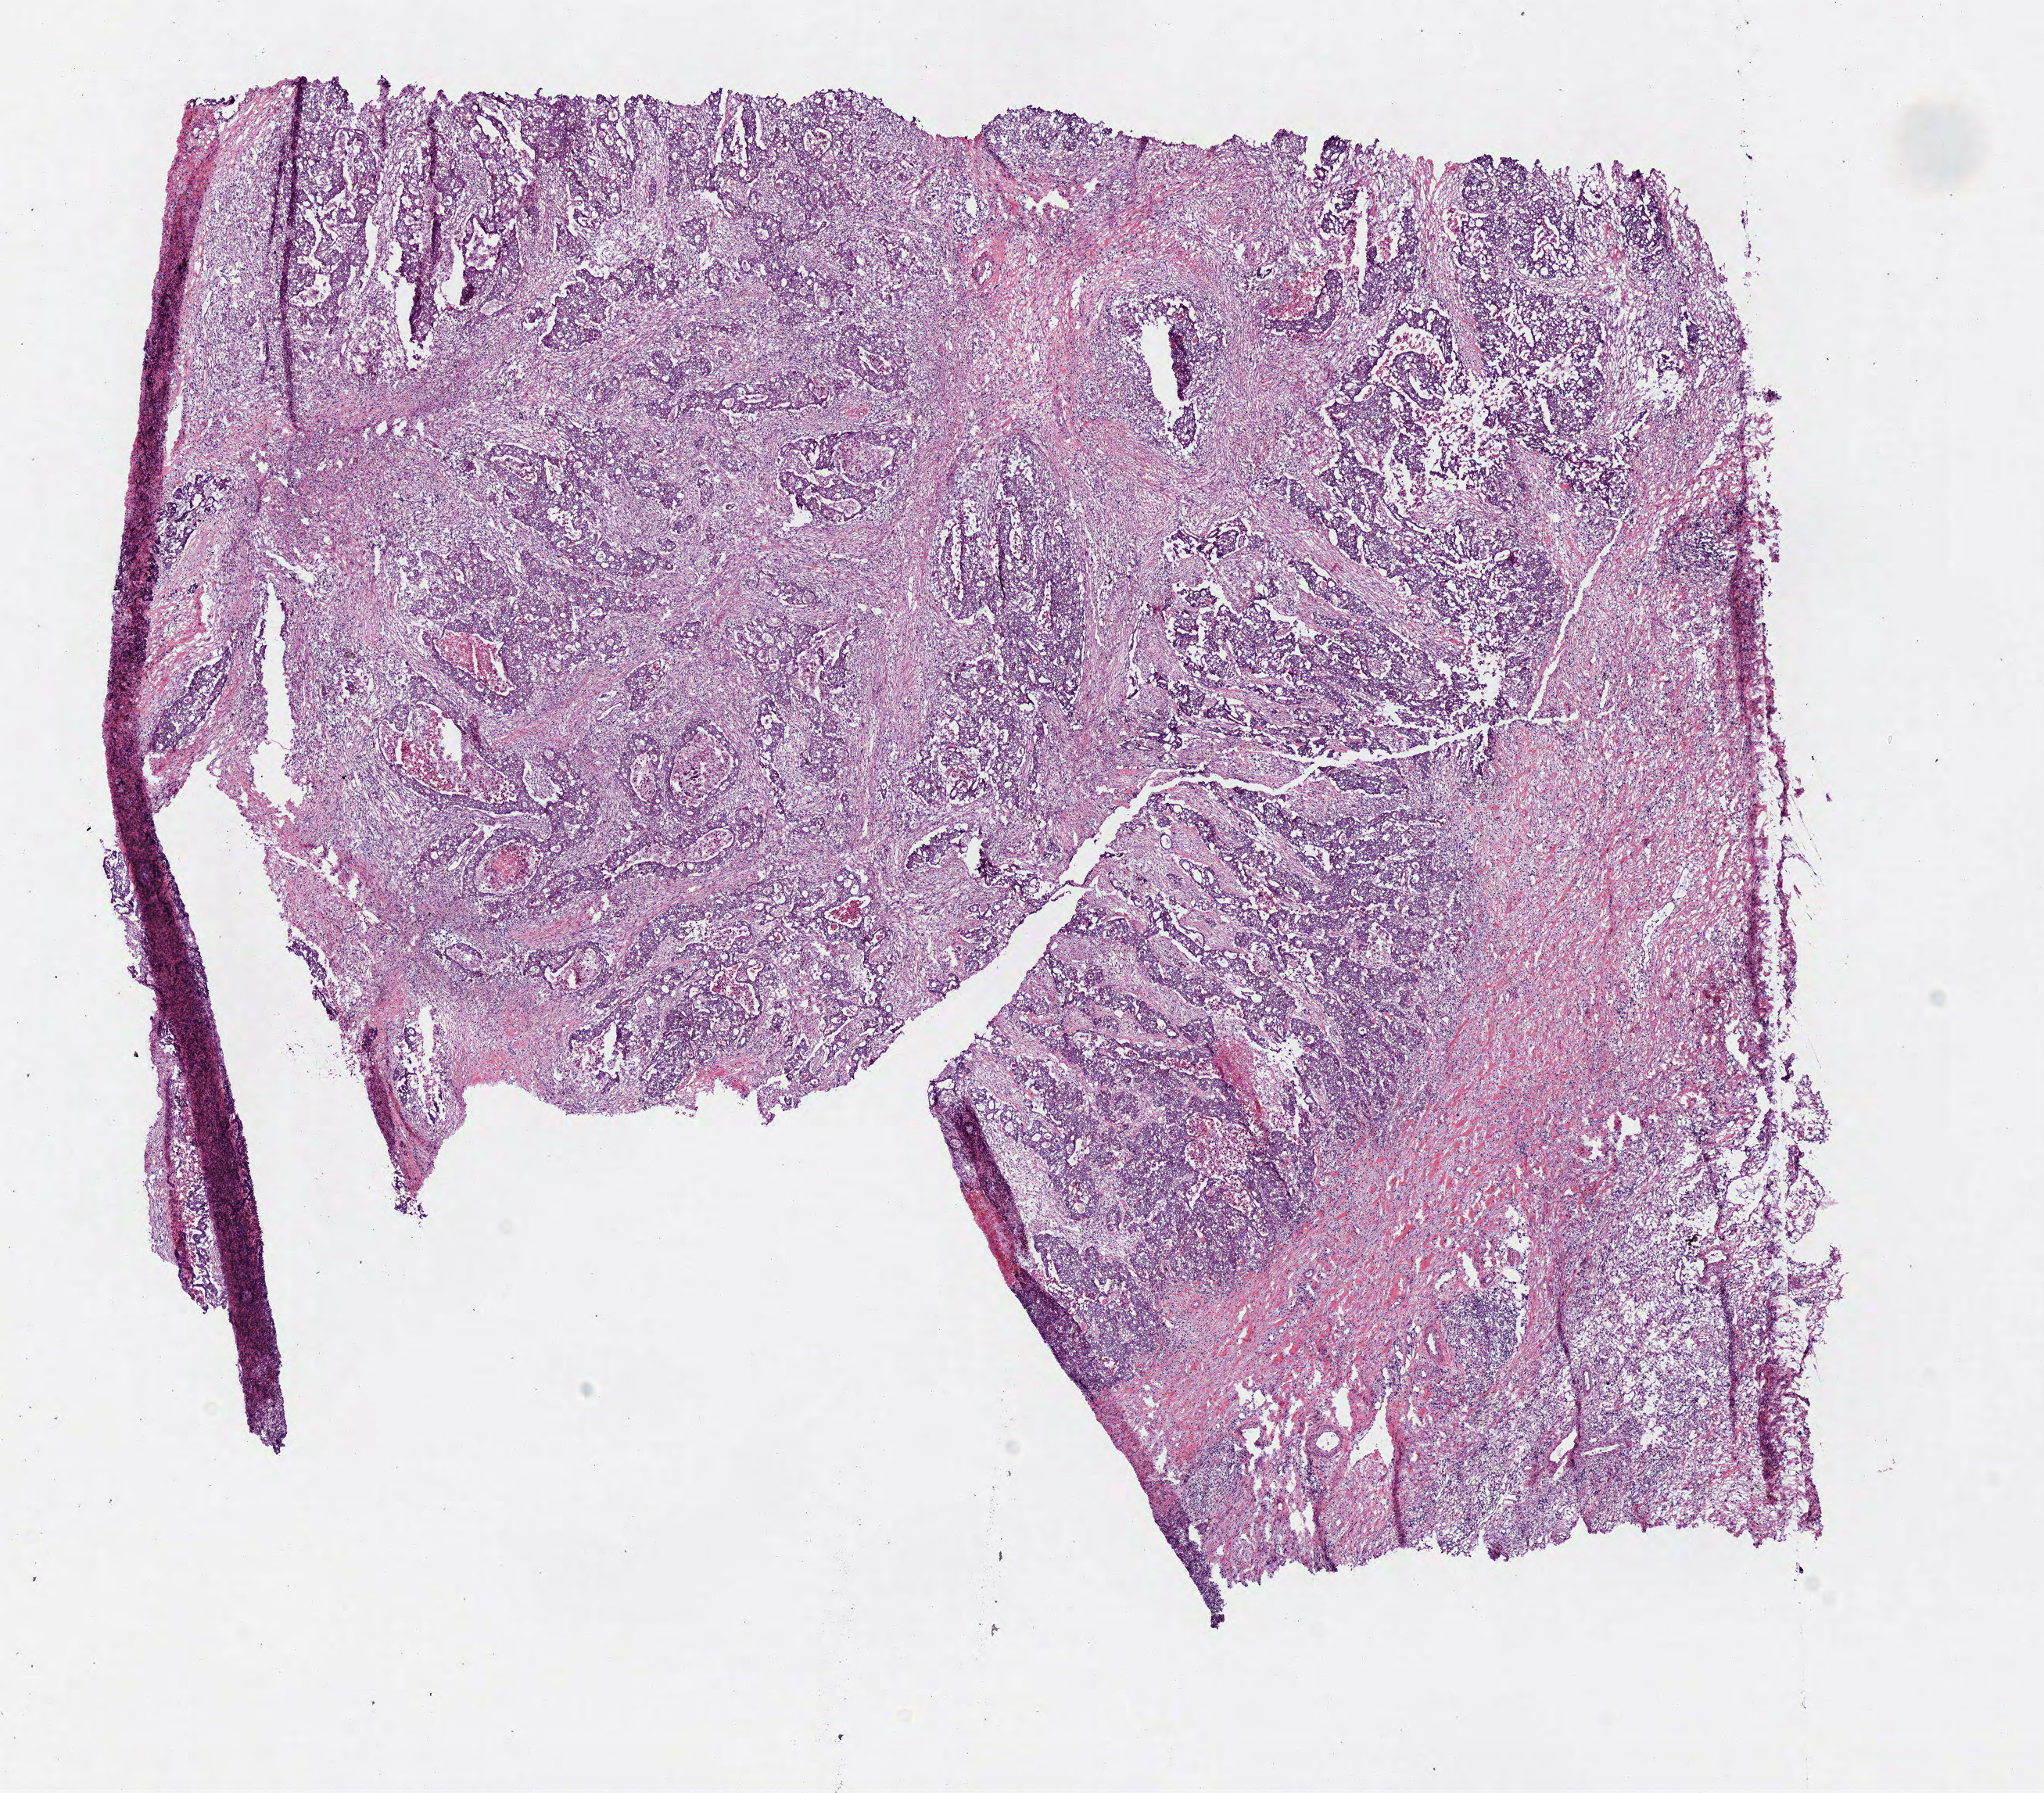
Hematoxylin and eosin (H&E) stained whole-slide image, shown as a low-resolution overview of the whole scanned area (about 10.3 x 9.0 mm, acquisition: 40x scan); frozen section from the bottom of the tissue portion; colon, primary tumour sample. Male patient; age at initial diagnosis 69 years. Slide review estimates, as recorded: tumour cells 60%, tumour nuclei 75%, normal cells 0%, stromal cells 30%, necrosis 10%.
• AJCC pathologic stage: IIIC (6th edition)
• diagnosis: Adenocarcinoma, NOS (descending colon)